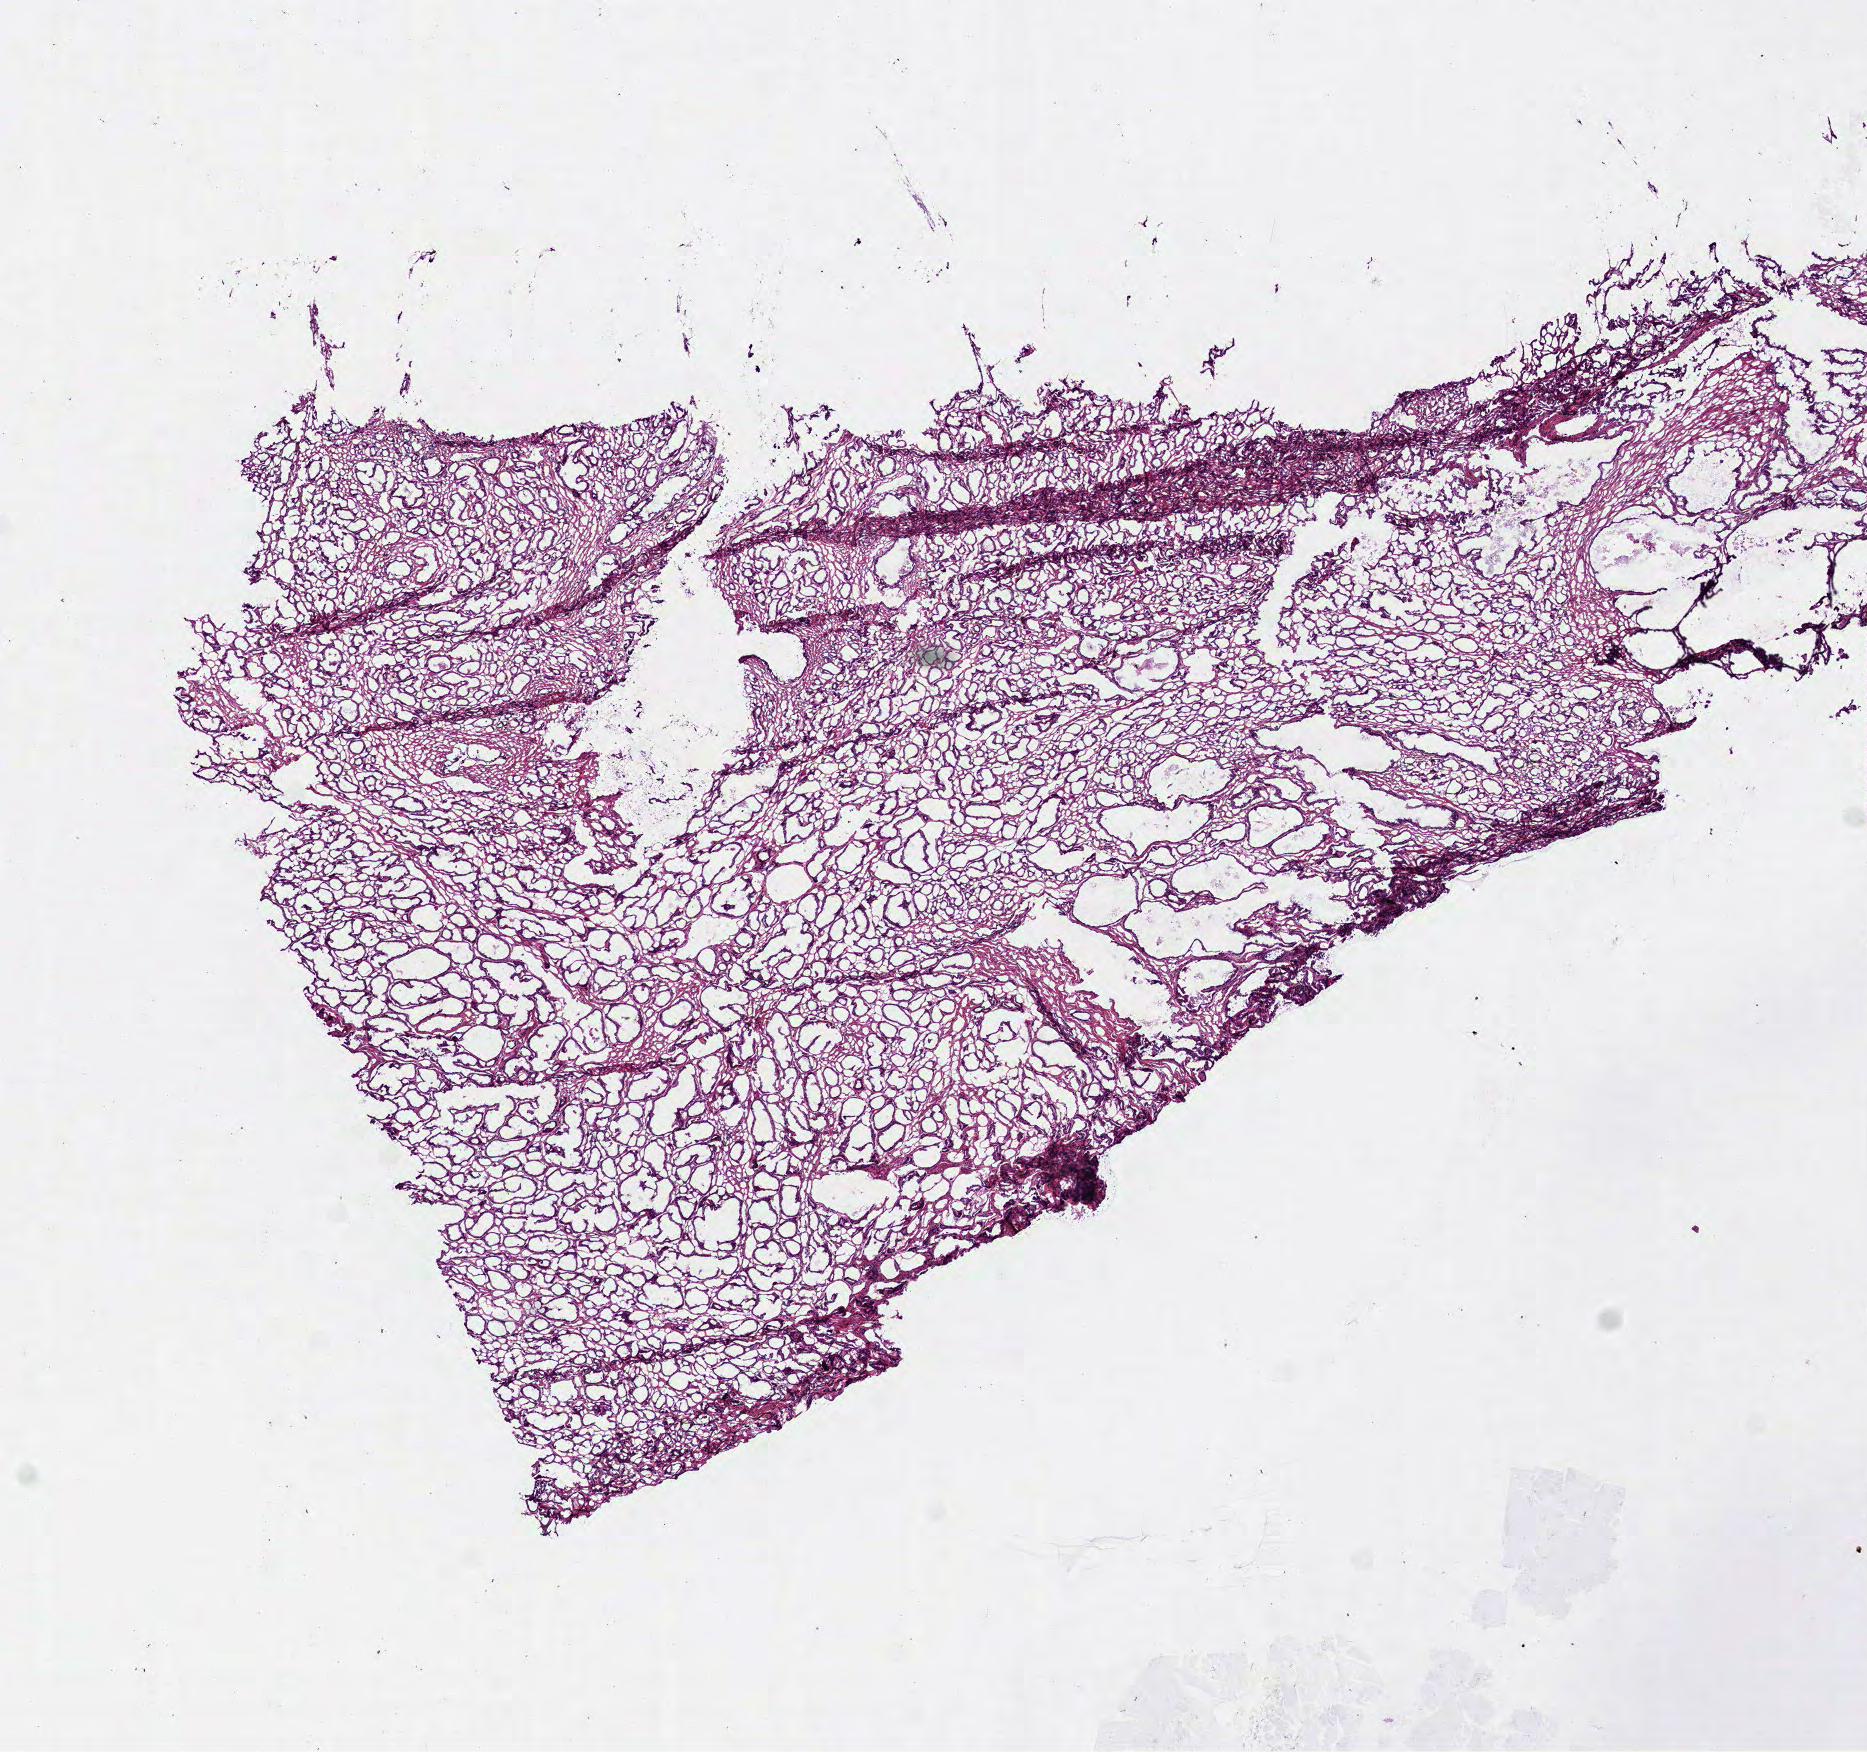
Digitized H&E-stained tissue section (whole slide) — shown as a low-resolution overview of the whole scanned area (about 7.5 x 7.1 mm); frozen section from the bottom of the tissue portion; primary tumour sample from the prostate. Patient: male, age at initial diagnosis 54 years. Composition of this section per pathologist review: tumour cells 75%, tumour nuclei 75%.
Pathologic diagnosis: Acinar cell carcinoma (prostate gland).